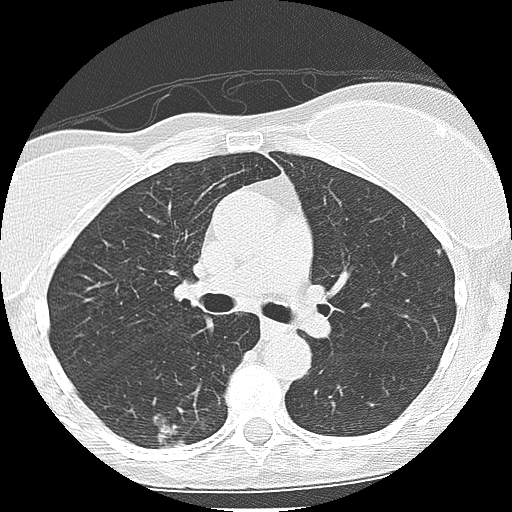
Low-dose screening chest CT, one axial slice; position 130 of 225 along the scan axis; reconstruction kernel LUNG; 120 kVp; lung window (W 1500 / L -600 HU); 2.5 mm slice thickness; 512 × 512 image matrix, field of view 300 × 300 mm.
Outlined on this slice (expert manual segmentation):
- lesion 1 (tumor, lower lobe of right lung): box from (x=158, y=423) to (x=184, y=448) px